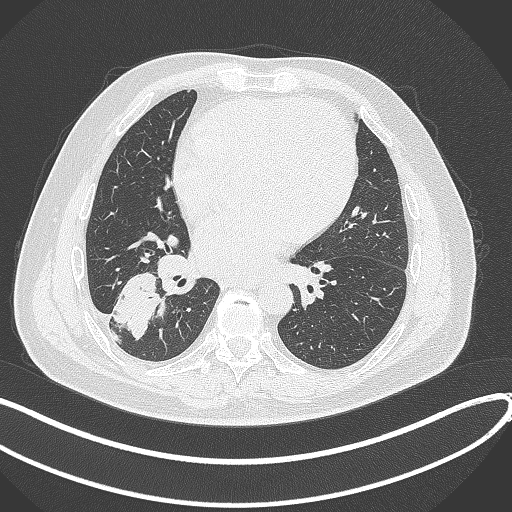
Chest CT, one axial slice. Position 158 of 360 along the scan axis. Reconstruction kernel B70f. Lung window (W 1500 / L -600 HU). 1 mm slice thickness. 512 × 512 image matrix, field of view 400 × 400 mm. Male patient, age 59 years.
Outlined on this slice (rectangle marked by the reading radiologist):
- lung tumour (recorded histology: adenocarcinoma): bounding box [x1, y1, x2, y2] px = [108, 262, 161, 343]